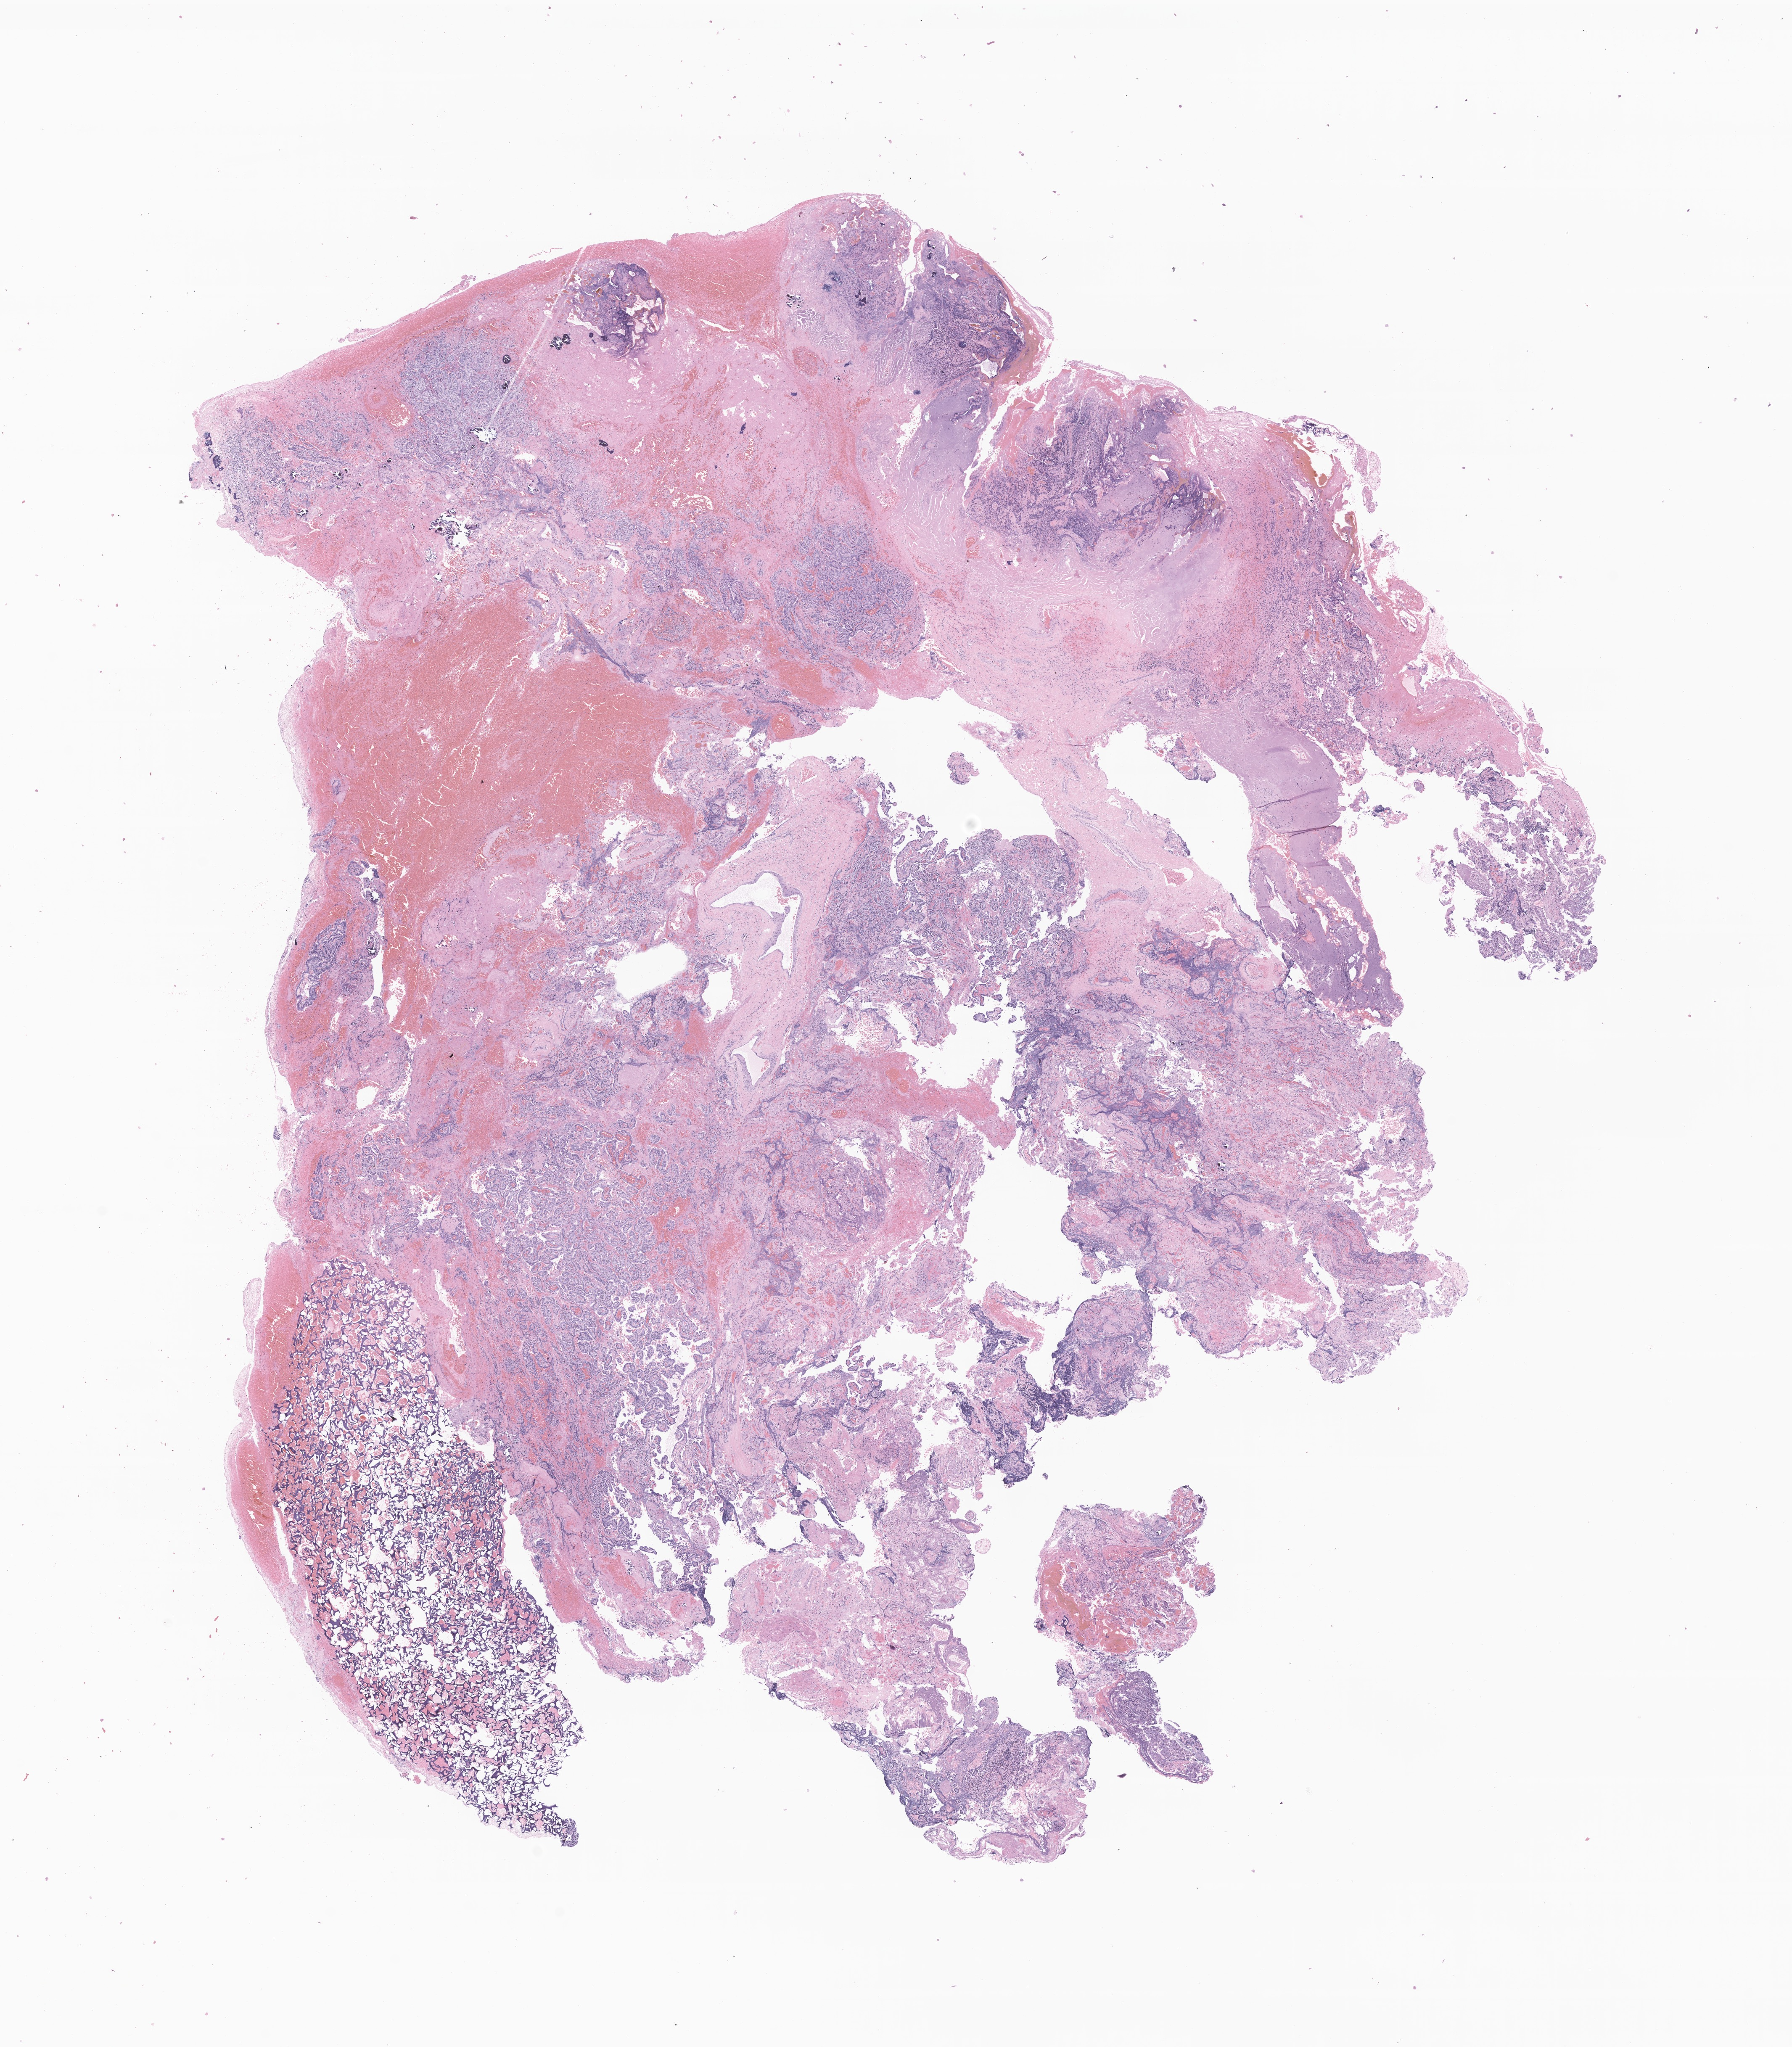
Digitized haematoxylin and eosin-stained section of tumor tissue from the brain, shown as a low-resolution overview of the whole scanned area (about 18.0 x 20.5 mm), formalin-fixed paraffin-embedded section. Patient: male, age 215 months (17 years 11 months).
• diagnosis (ICD-O-3 morphology term): Ependymoma, NOS